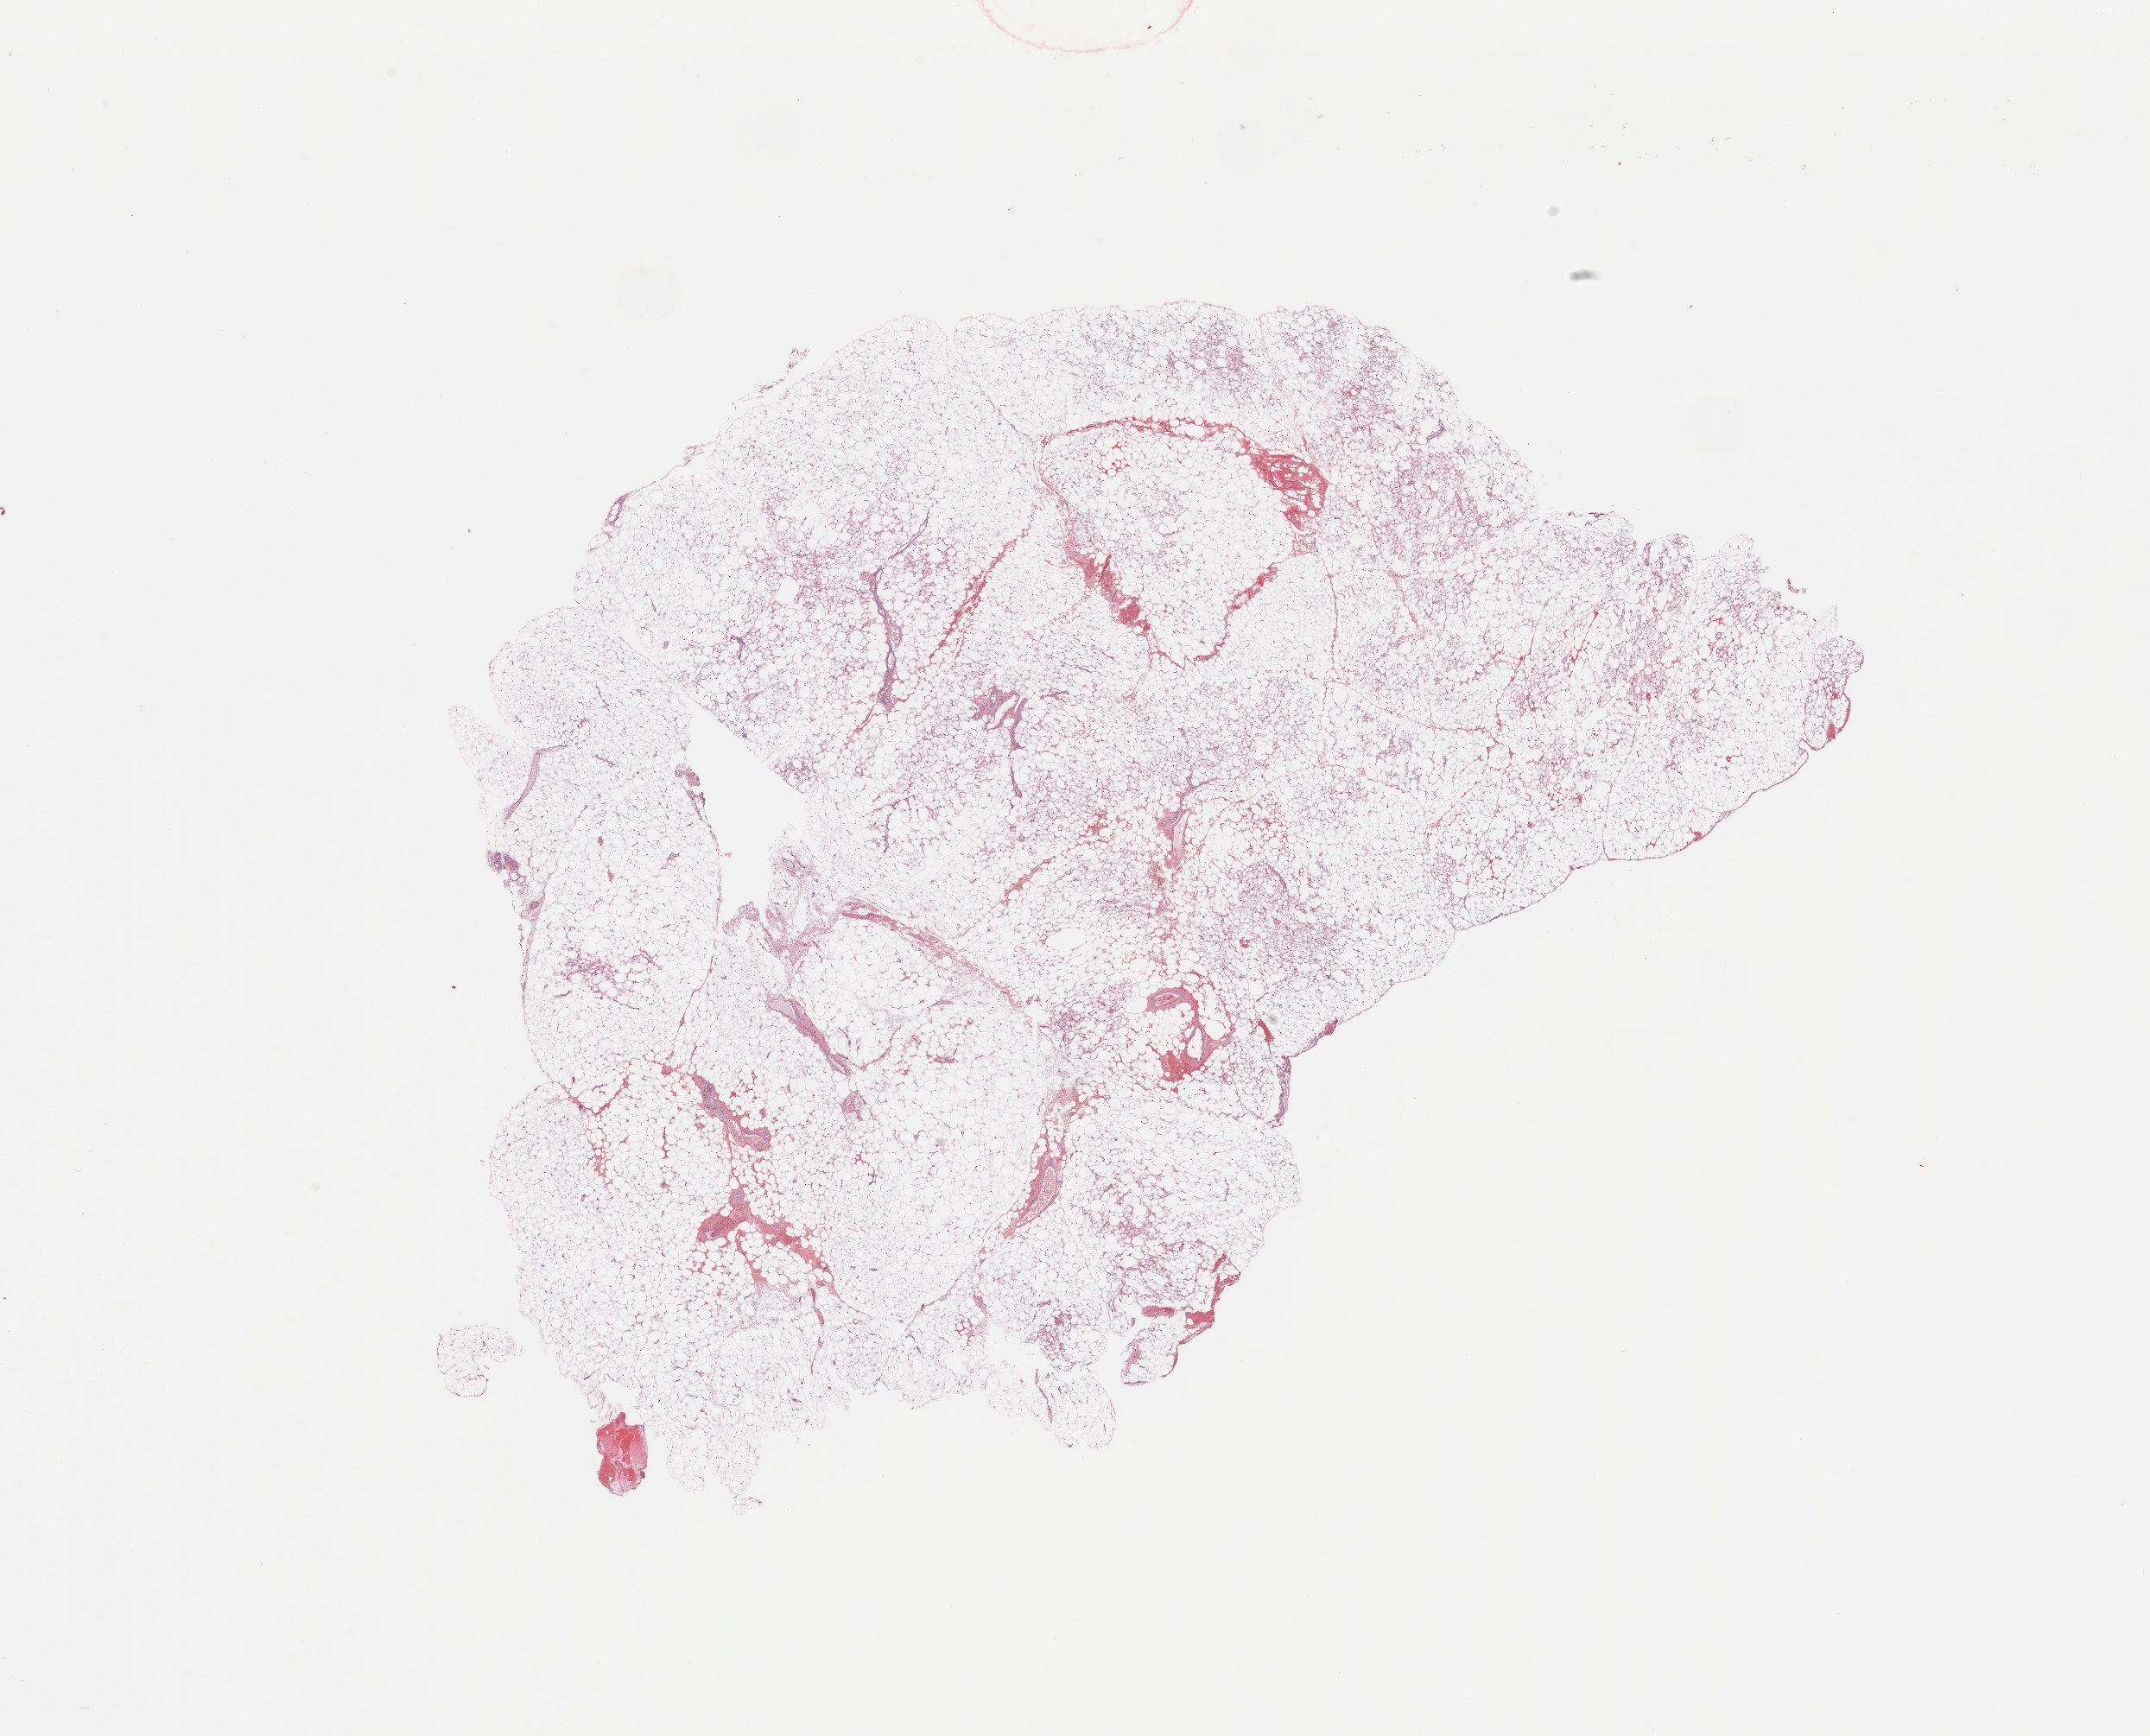
Whole-slide histology image, H&E — whole scanned area (about 19.7 x 15.9 mm) shown as a low-resolution overview; normal (non-tumour) tissue sample, kidney. Patient: male, age 51 years.
This section: normal (non-tumour) tissue from the same patient. Patient diagnosis: Renal cell carcinoma, NOS.